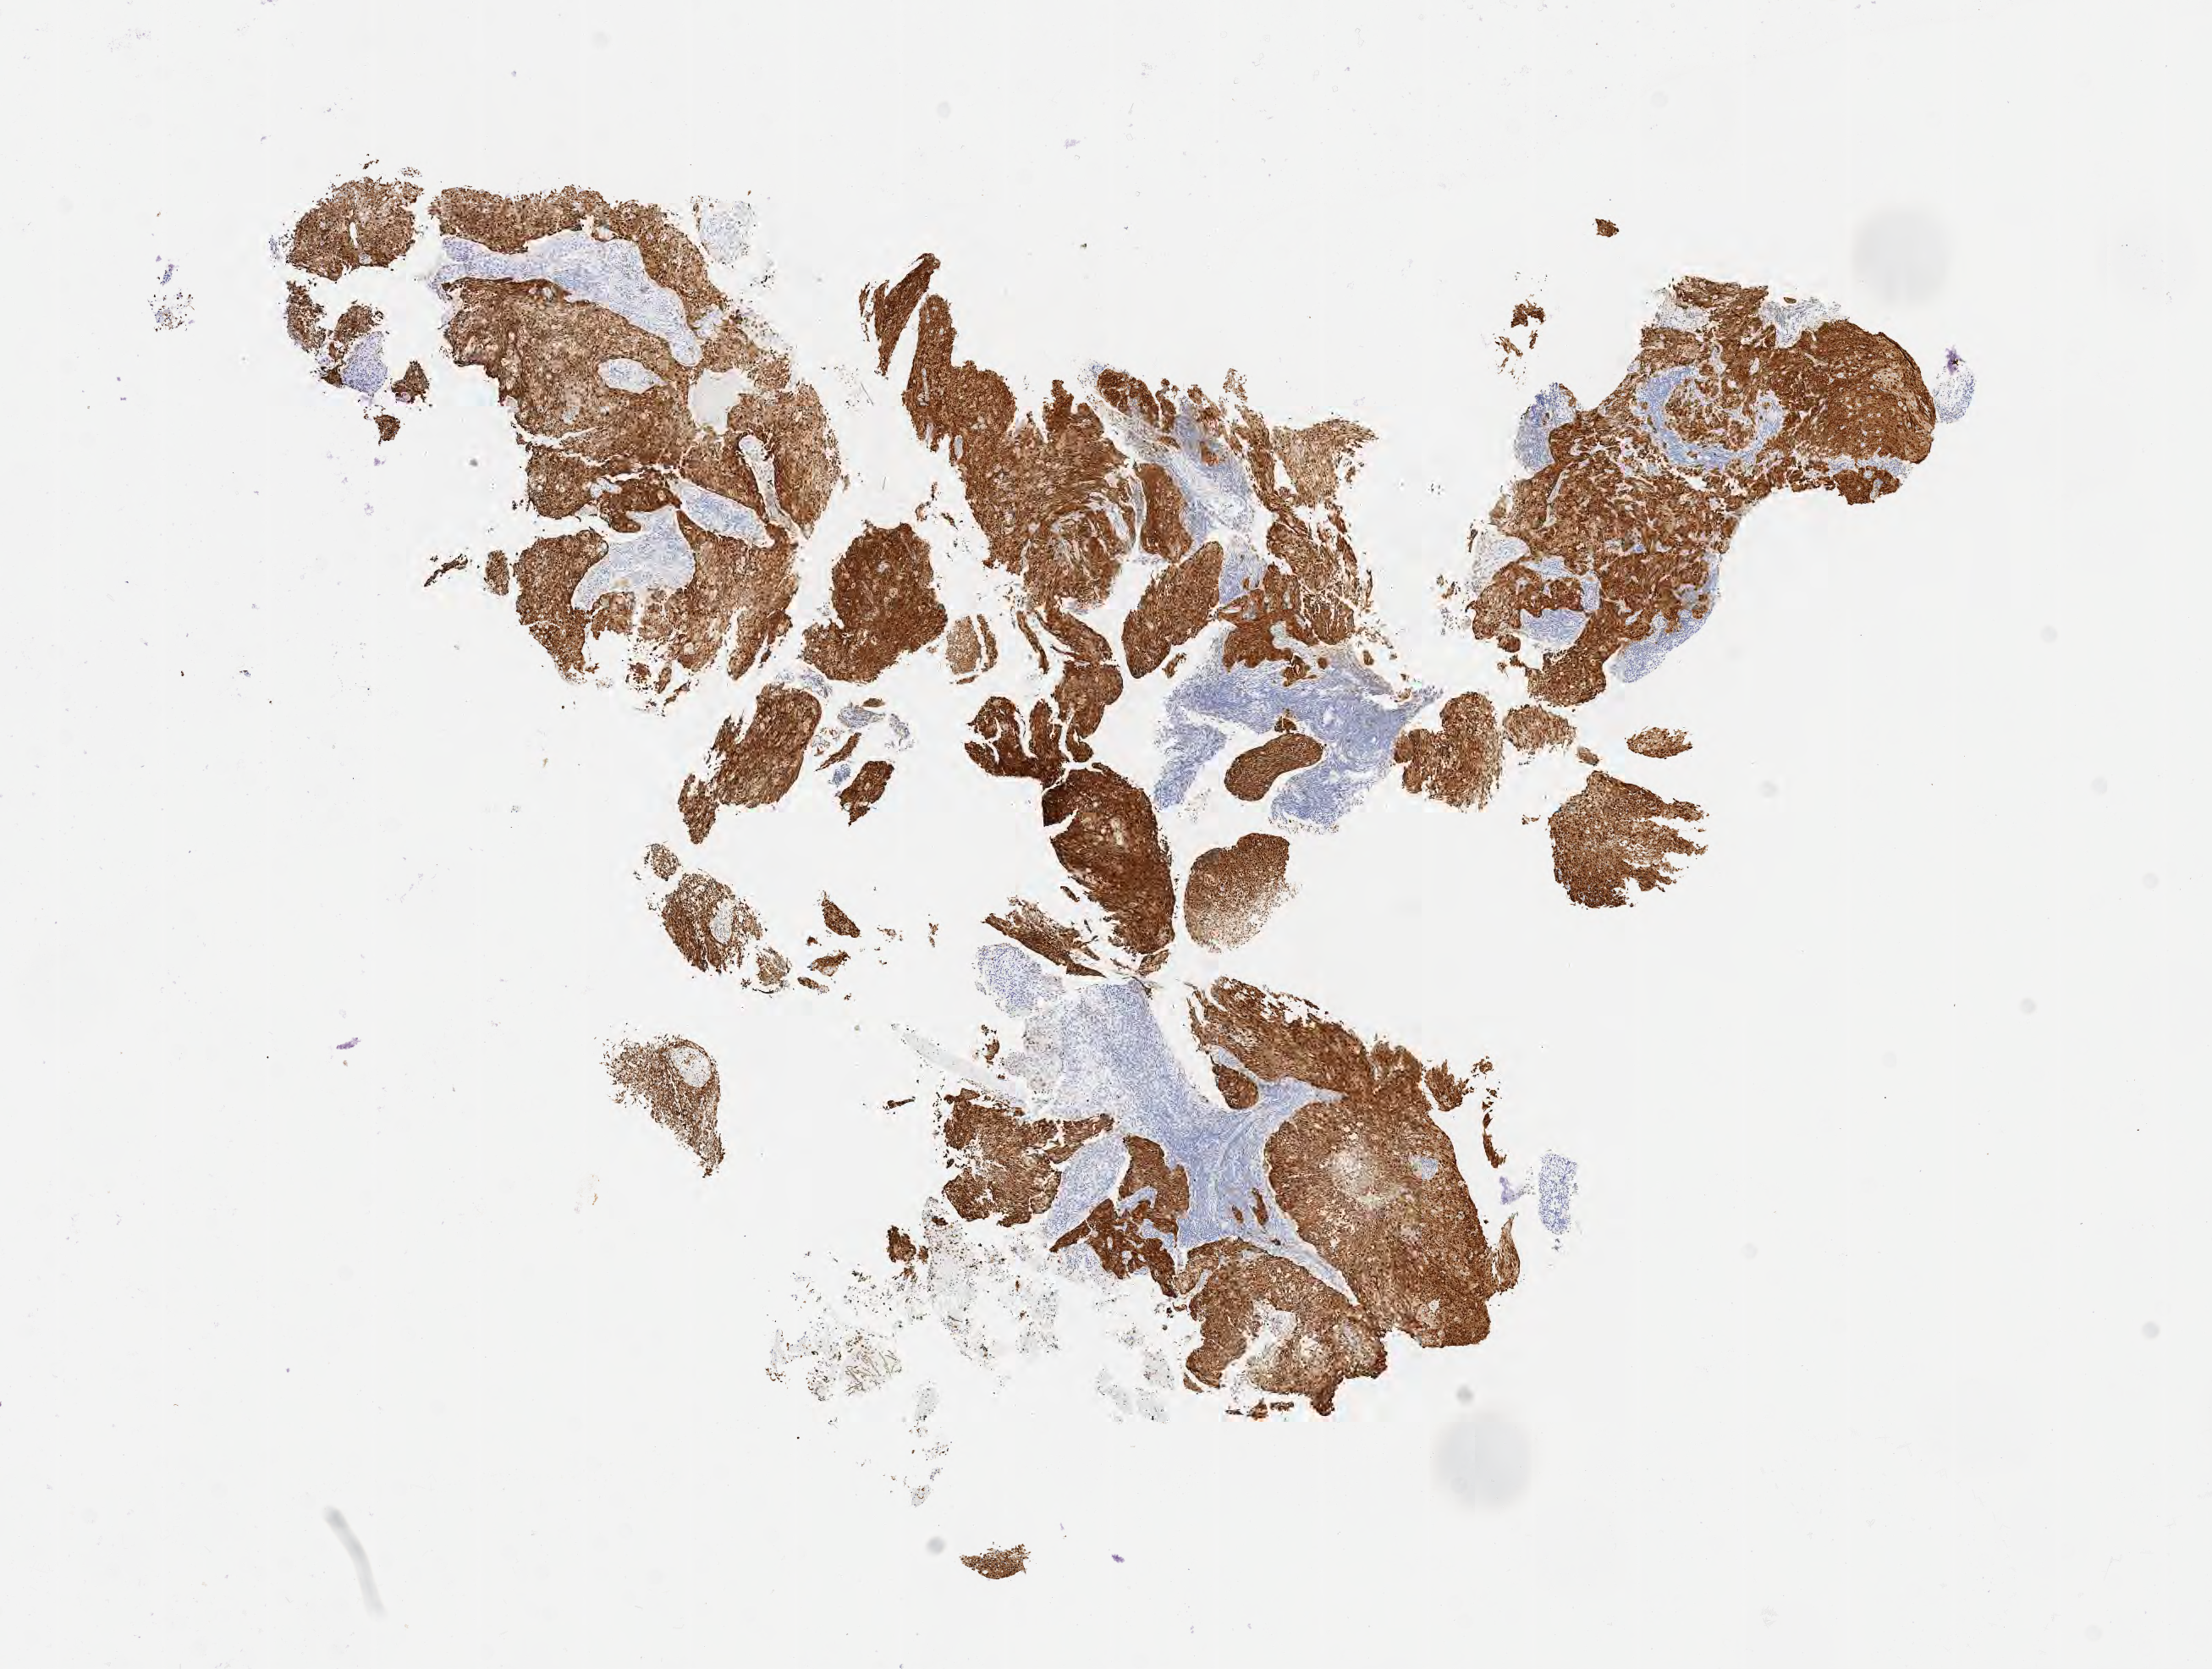
IHC for p16 (p16INK4a), whole-slide image, low-resolution overview of the scanned area, about 10.6 x 8.0 mm; specimen: tumor tissue; anatomic site: cervix. Patient female; age 57 years.
- histologic diagnosis: Squamous cell carcinoma, large cell, nonkeratinizing, NOS